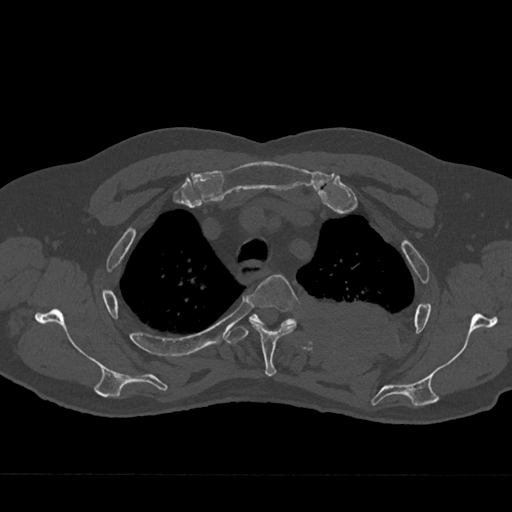
CT including the spine, one axial slice. Slice 551 of 797 in the series (ordered by position). Reconstruction kernel Br40s/3. Bone window (W 1800 / L 400 HU). 0.5 mm slice thickness. 512 × 512 image matrix, field of view 377 × 377 mm. Male patient, age 75 years. Case-level facts recorded for this patient, not image findings: primary cancer: renal; vertebrae with lytic lesions (as recorded): T4.
Structures marked on this image (semi-automatically segmented with operator editing):
- T3 vertebra: bounding box [x1, y1, x2, y2] px = [248, 275, 300, 377]
- T4 vertebra: [225, 314, 297, 344]